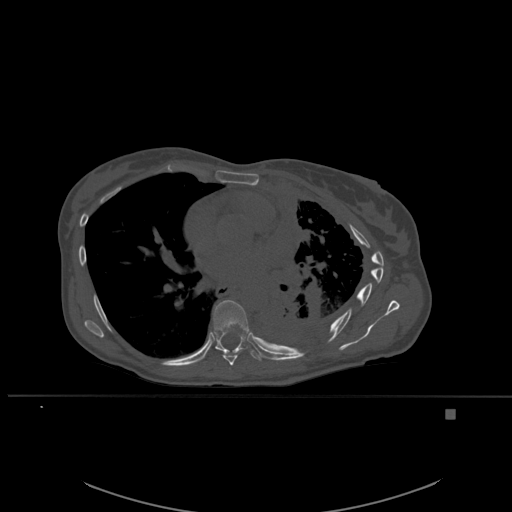
CT including the spine, one axial slice. Position 358 of 537 along the scan axis. Bone window (W 1800 / L 400 HU). 1.5 mm slice thickness. 512 × 512 image matrix, field of view 440 × 440 mm. Patient: female, 45 years. From the clinical record (not read from this slice): primary cancer: lung.
Structures marked on this image (semi-automatically segmented with operator editing):
- T7 vertebra: box from (x=217, y=349) to (x=244, y=366) px
- T8 vertebra: (x=213, y=300)–(x=262, y=360)